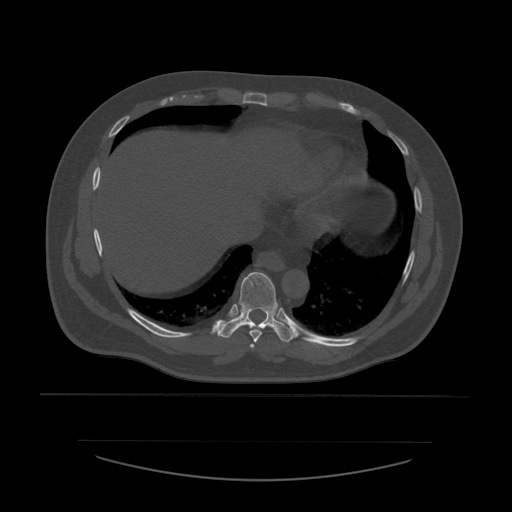
CT including the spine, one axial slice; position 323 of 532 along the scan axis; reconstruction kernel STANDARD; 120 kVp; bone window (W 1800 / L 400 HU); 512 × 512 image matrix, field of view 441 × 441 mm. Patient age 44 years. Case-level facts recorded for this patient, not image findings: primary cancer: soft tissue sarcoma.
Annotated regions visible in this slice (semi-automatically segmented with operator editing):
- T7 vertebra: box from (x=250, y=344) to (x=255, y=349) px
- T8 vertebra: (x=249, y=330)–(x=263, y=343)
- T9 vertebra: (x=217, y=272)–(x=296, y=343)